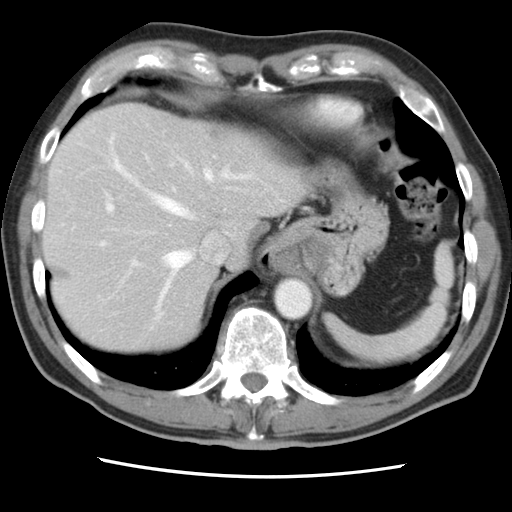
Contrast-enhanced abdominal CT, one axial slice; position 67 of 83 along the scan axis; intravenous contrast given; soft-tissue window (W 400 / L 40 HU); 5 mm slice thickness; 512 × 512 image matrix. Male patient, age 69 years. From the clinical record (not read from this slice): diagnosis: colorectal cancer liver metastases, imaged before liver resection; multiple liver metastases: yes; largest metastasis: 3.5 cm.
Structures marked on this image (expert manual segmentation):
- hepatic veins: bounding box [x1, y1, x2, y2] px = [108, 133, 247, 315]
- liver: [44, 103, 297, 353]
- planned liver remnant (the part of the liver to remain after resection): [44, 146, 216, 353]
- portal vein (with intrahepatic branches): [100, 187, 176, 266]